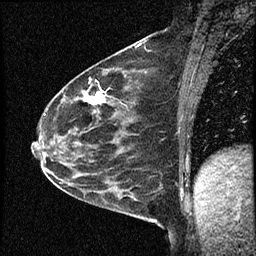
Breast MRI (dynamic contrast-enhanced), one sagittal slice. Position 33 of 60 along the scan axis. Dynamic contrast-enhanced study with each time point stored as its own series, time point 2 of 4 at this slice position (early post-contrast, ordered by acquisition time). 1.5 T. TE 4.2 ms, TR 17.6 ms. 256 × 256 image matrix, field of view 200 × 200 mm. Female patient, age 53 years. Case-level facts recorded for this patient, not image findings: setting: breast cancer imaged before/during neoadjuvant chemotherapy; receptor status: HR-positive, HER2-negative.
Structures marked on this image (semi-automatic segmentation, software-assisted and operator-edited):
- analysis volume of interest (the breast-tissue region the enhancement analysis was run in; not a lesion): bounding box <42,69,156,199> (left, top, right, bottom; pixels)
- tumour enhancement mask (voxels above the 100 % enhancement threshold inside the analysis volume of interest): <83,91,105,105>